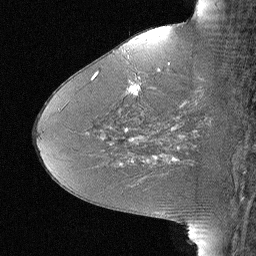
Breast MRI (dynamic contrast-enhanced), one sagittal slice. Slice 28 of 64 in the series (ordered by position). Dynamic contrast-enhanced study with each time point stored as its own series, time point 2 of 3 at this slice position (early post-contrast, ordered by acquisition time). 1.5 T. TE 4 ms, TR 30 ms. 2.25 mm slice thickness. 256 × 256 image matrix, field of view 180 × 180 mm. Female patient, age 46 years. From the clinical record (not read from this slice): setting: breast cancer imaged before/during neoadjuvant chemotherapy; receptor status: HR-positive, HER2-negative.
Annotated regions visible in this slice (semi-automatically segmented with operator editing):
- analysis volume of interest (the breast-tissue region the enhancement analysis was run in; not a lesion): box from (x=106, y=43) to (x=184, y=119) px
- tumour enhancement mask (voxels above the 90 % enhancement threshold inside the analysis volume of interest): (x=129, y=85)–(x=140, y=96)